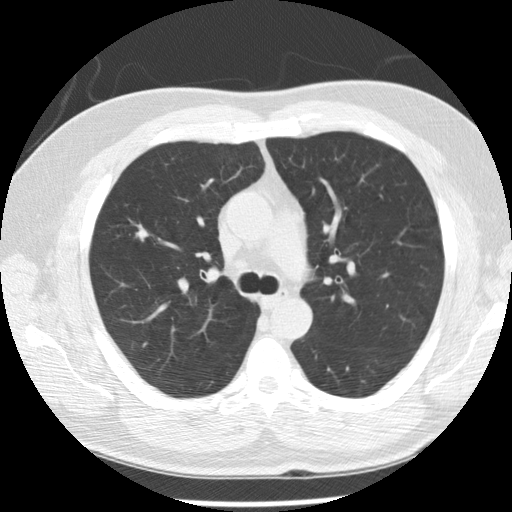
Chest CT (low-dose screening protocol), one axial image; first (baseline) screen; lung window (W 1500 / L -600 HU); standard (soft-tissue) reconstruction kernel (STANDARD); 512 × 512 image matrix. Male participant, aged 57 years at enrolment. Former smoker at enrolment.
Expert reader's lesion annotation, bounding box <124,220,157,252> (left, top, right, bottom; pixels). The exam's reader record, not a measurement of the box and not confirmed to be the same lesion: non-calcified nodule or mass ≥4 mm, right upper lobe, 7 × 7 mm, poorly defined margins, soft tissue attenuation. Later outcome: lung cancer diagnosed 125 days after this screen — squamous cell carcinoma, NOS, right upper lobe, moderately differentiated (G2), stage IA (AJCC 6th edition), 10 mm at pathology.